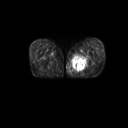
FDG PET of an extremity soft-tissue mass (from a PET/CT study), one axial slice. Slice 18 of 267 in the series (ordered by position). 3.27 mm slice thickness. 128 × 128 image matrix, field of view 600 × 600 mm. Male patient, age 59 years. From the clinical record (not read from this slice): histological type: pleiomorphic liposarcoma; grade: high; site of the primary tumour: left thigh.
Annotated regions visible in this slice (expert contour drawn on MRI and transferred to this co-registered scan by the dataset authors):
- gross tumour volume including surrounding oedema: box from (x=72, y=53) to (x=90, y=72) px
- gross tumour volume (mass): (x=73, y=58)–(x=87, y=71)